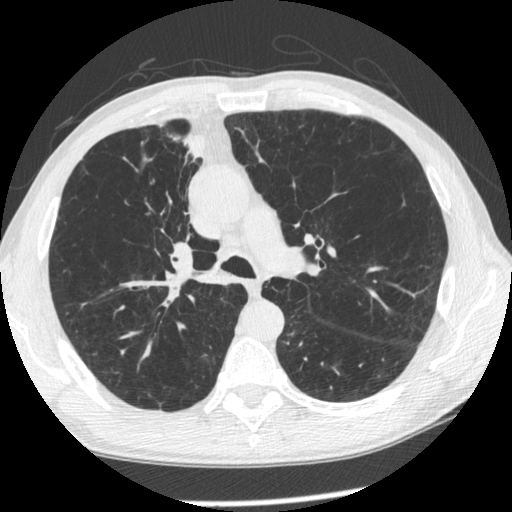
Low-dose screening chest CT, one axial slice; 120 kVp; lung window (W 1500 / L -600 HU); 1.25 mm slice thickness; 512 × 512 image matrix.
Annotated regions visible in this slice (expert manual segmentation):
- lesion 1 (tumor, upper lobe of right lung): bounding box <183,134,204,158> (left, top, right, bottom; pixels)